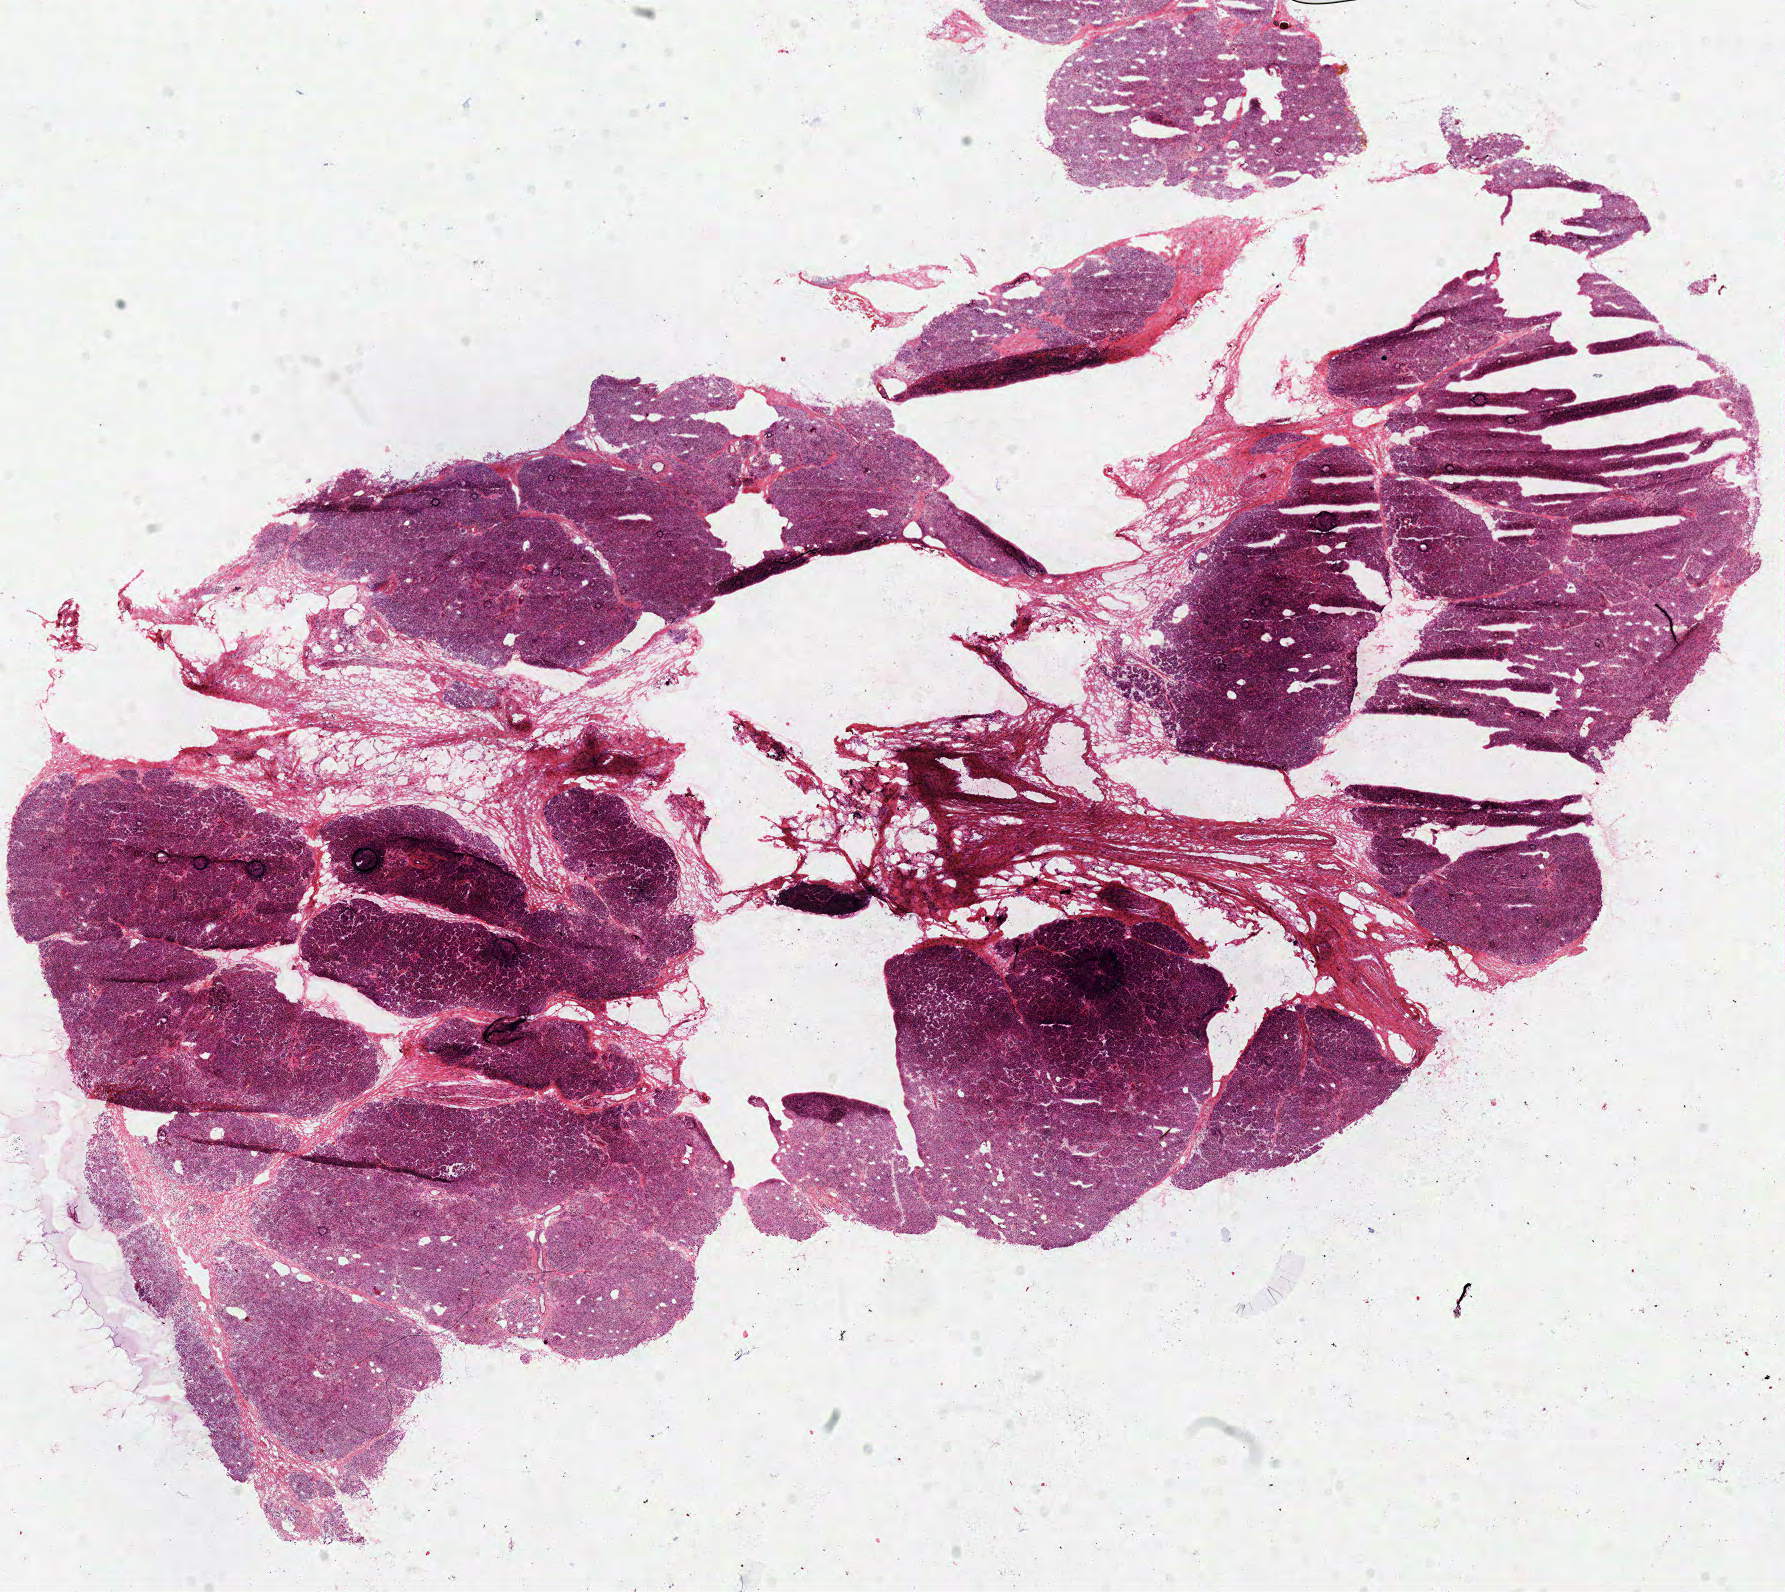
Whole-slide histology image, Hematoxylin and eosin (H&E) stained — low-resolution overview of the scanned area, about 14.1 x 12.5 mm; frozen section from the top of the tissue portion; solid tissue normal (non-tumour tissue) sample from the pancreas. Male patient; age at initial diagnosis 71 years.
• this section: solid tissue normal sample (biorepository sample class)
• patient diagnosis: Infiltrating duct carcinoma, NOS (head of pancreas)